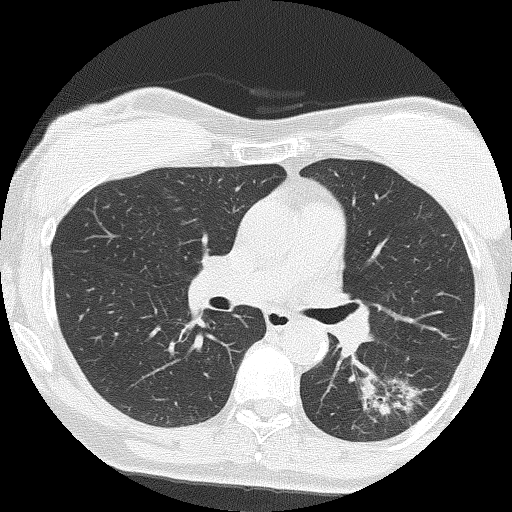
Chest CT (low-dose screening protocol), one axial image; second annual screen; lung window (W 1500 / L -600 HU); lung (sharp) reconstruction kernel (FC51); 120 kVp; 512 × 512 image matrix. Female participant, aged 64 years at enrolment. Former smoker at enrolment.
- Expert-annotated lung lesion, bounding box [x1, y1, x2, y2] px = [358, 368, 440, 438].
- The screening reader recorded 3 non-calcified nodules or masses ≥4 mm on this exam (right upper lobe, right upper lobe, right middle lobe); which of them this box marks is not recorded.